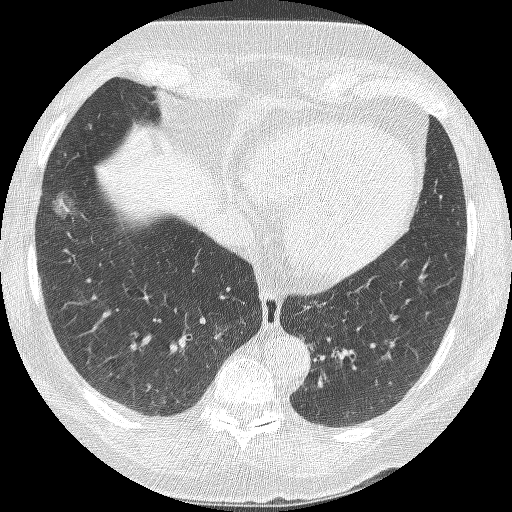
Low-dose screening chest CT, axial slice. Second screening round (one year after baseline). Lung window (W 1500 / L -600 HU). 1.25 mm slice thickness. Lung (sharp) reconstruction kernel (BONE). 512 × 512 image matrix, field of view 310 × 310 mm. Female, age 68 years at enrolment. Current smoker at enrolment.
Expert reader's lesion annotation, bounding box <35,190,79,242> (left, top, right, bottom; pixels). Screening reader's record for this exam (one nodule recorded; not confirmed to be the boxed lesion): non-calcified nodule or mass ≥4 mm, right lower lobe, 18 × 15 mm, poorly defined margins, ground glass attenuation, pre-existing on the prior screen: yes; interval growth: yes. Official screen result: positive, other. Lung cancer was diagnosed 42 days after this screen: bronchiolo-alveolar adenocarcinoma, NOS, right lower lobe, well differentiated (G1), stage IA (AJCC 6th edition), 13 mm at pathology.